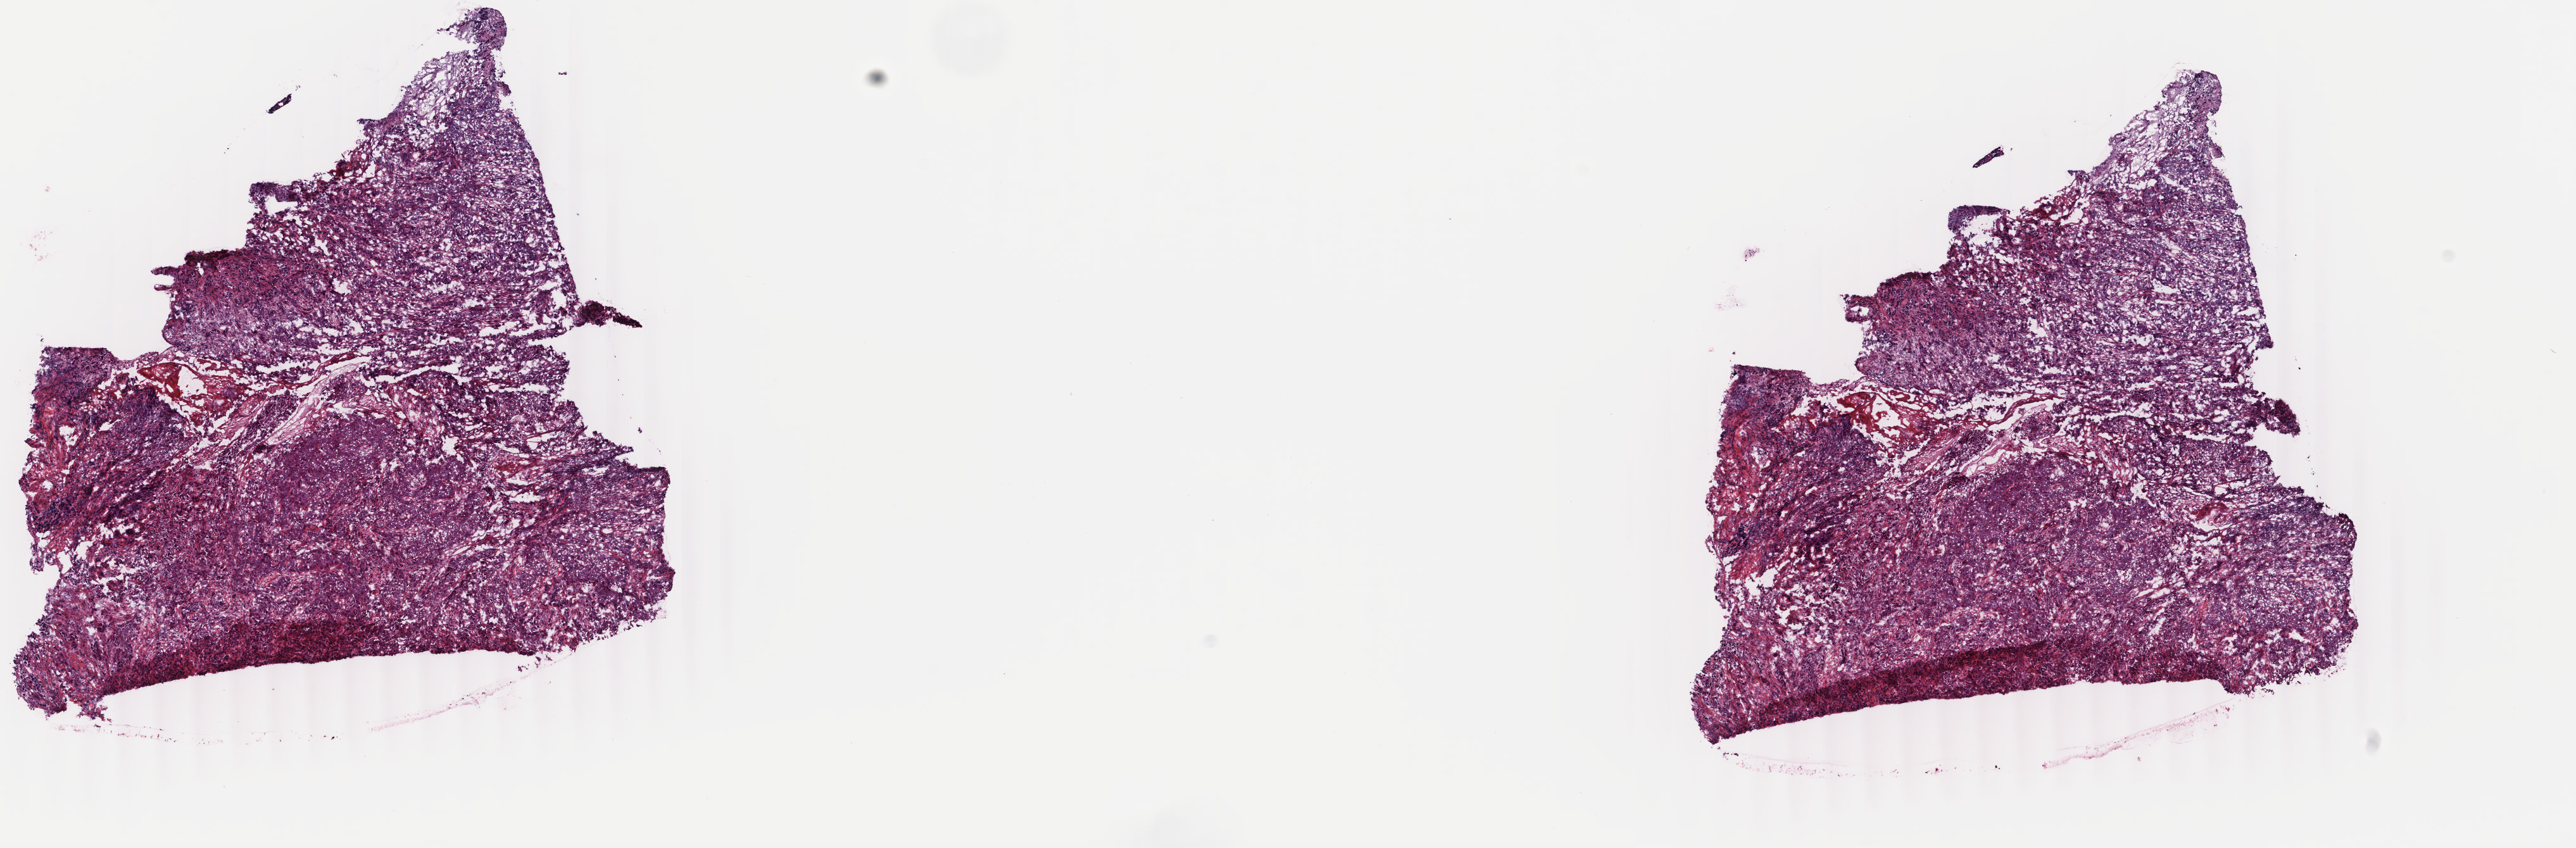
Whole-slide histology image, Hematoxylin and eosin (H&E) stained, a low-resolution overview of the entire scanned area, about 16.2 x 5.3 mm. Frozen section from the top of the tissue portion. Cervix, primary tumour sample. Female, age 20 years at initial diagnosis. Histologic grade: G3 (poorly differentiated). Slide review estimates, as recorded: tumour cells 80%, tumour nuclei 70%, normal cells 2%, stromal cells 15%, necrosis 3%. Inflammatory infiltration, as recorded: lymphocyte infiltration 20%, monocyte infiltration 0%, neutrophil infiltration 0%.
FIGO stage: IB2. Histologic diagnosis: Squamous cell carcinoma, large cell, nonkeratinizing, NOS.